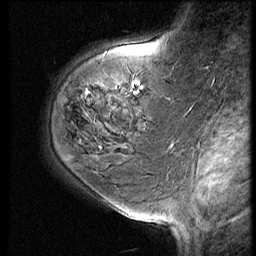
Breast MRI (dynamic contrast-enhanced), one sagittal slice; slice 20 of 60 in the series (ordered by position); 3 images stored at this slice position (order not interpretable as contrast timing); 1.5 T; TE 4.2 ms, TR 9 ms; 256 × 256 image matrix, field of view 180 × 180 mm. Female patient, age 59 years. From the clinical record (not read from this slice): setting: breast cancer imaged before/during neoadjuvant chemotherapy; receptor status: HER2-positive.
Structures marked on this image (semi-automatically segmented with operator editing):
- analysis volume of interest (the breast-tissue region the enhancement analysis was run in; not a lesion): box from (x=78, y=61) to (x=161, y=125) px
- tumour enhancement mask (voxels above the 140 % enhancement threshold inside the analysis volume of interest): (x=87, y=92)–(x=90, y=96)